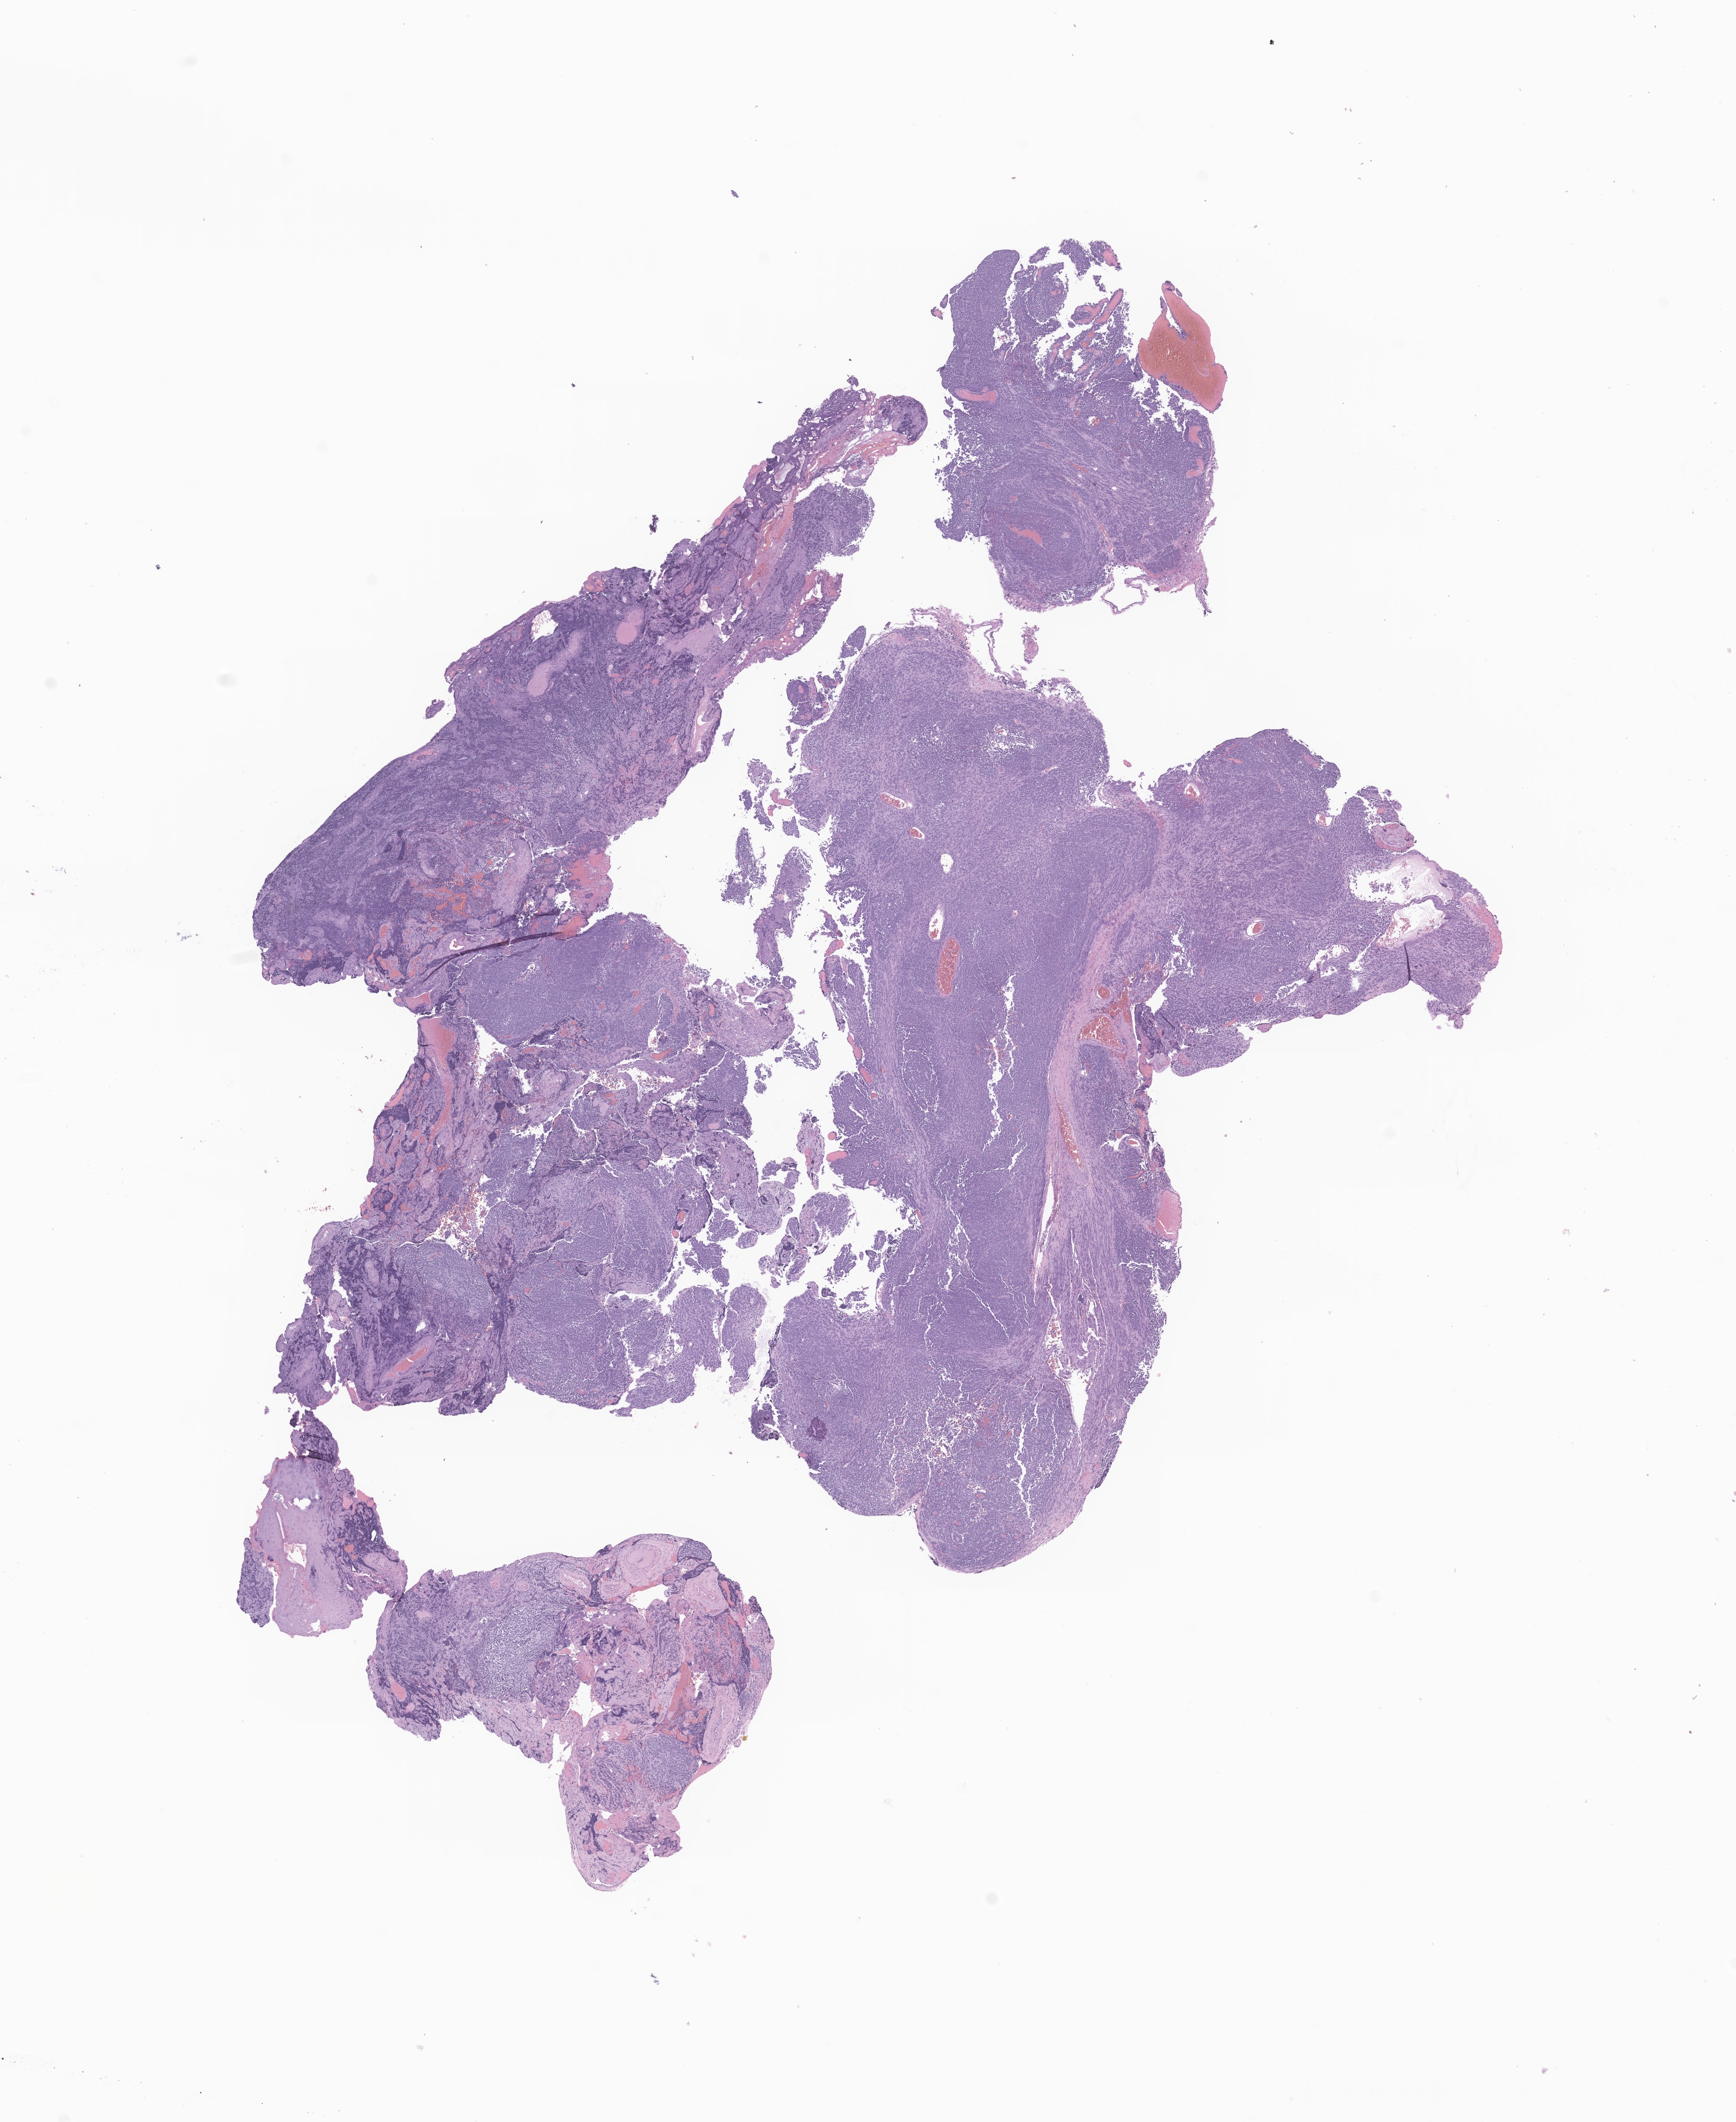
Whole-slide image, haematoxylin and eosin stain of tumor tissue from the brain, low-resolution overview of the scanned area, about 13.8 x 16.9 mm; FFPE section. Patient female; age 139 months (11 years 7 months).
Recorded diagnosis: Medulloblastoma, NOS.